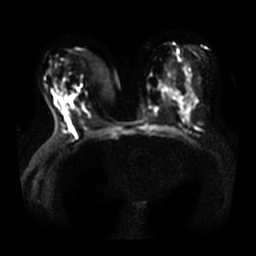
Breast MRI, one axial slice. Position 17 of 33 along the scan axis. Diffusion-weighted series; image 2 of 4 stored at this slice position (different b-values; order by instance number). 3 T. 5 mm slice thickness. 256 × 256 image matrix, field of view 360 × 360 mm. Female patient.
Annotated regions visible in this slice (expert manual segmentation):
- tumour on diffusion-weighted imaging: box from (x=73, y=86) to (x=80, y=93) px